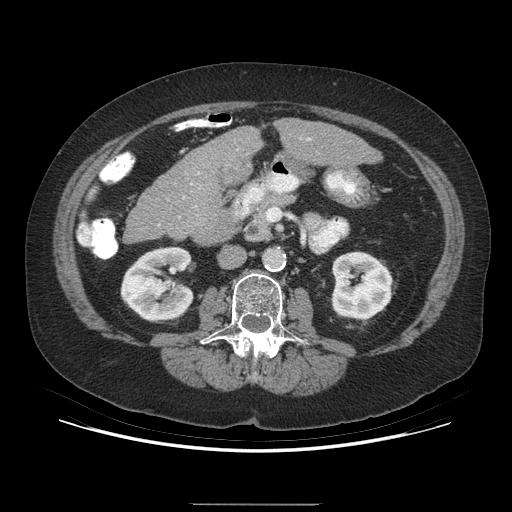
Contrast-enhanced abdominal CT (liver protocol), one axial slice. Position 135 of 192 along the scan axis. Reconstruction kernel STANDARD. Soft-tissue window (W 400 / L 40 HU). 2.5 mm slice thickness. 512 × 512 image matrix. Case-level facts recorded for this patient, not image findings: diagnosis: hepatocellular carcinoma (patient treated with transarterial chemoembolisation; whether this scan precedes or follows treatment is not stated here); TNM stage (as recorded): Stage-I; Child-Pugh class: A; tumour differentiation: moderately differentiated.
Structures marked on this image (semi-automatically segmented with operator editing):
- liver parenchyma outside the tumour (the mass and vessels are separate outlines, so this box may not span the whole liver): bounding box <128,118,382,242> (left, top, right, bottom; pixels)
- mass: <217,157,252,185>